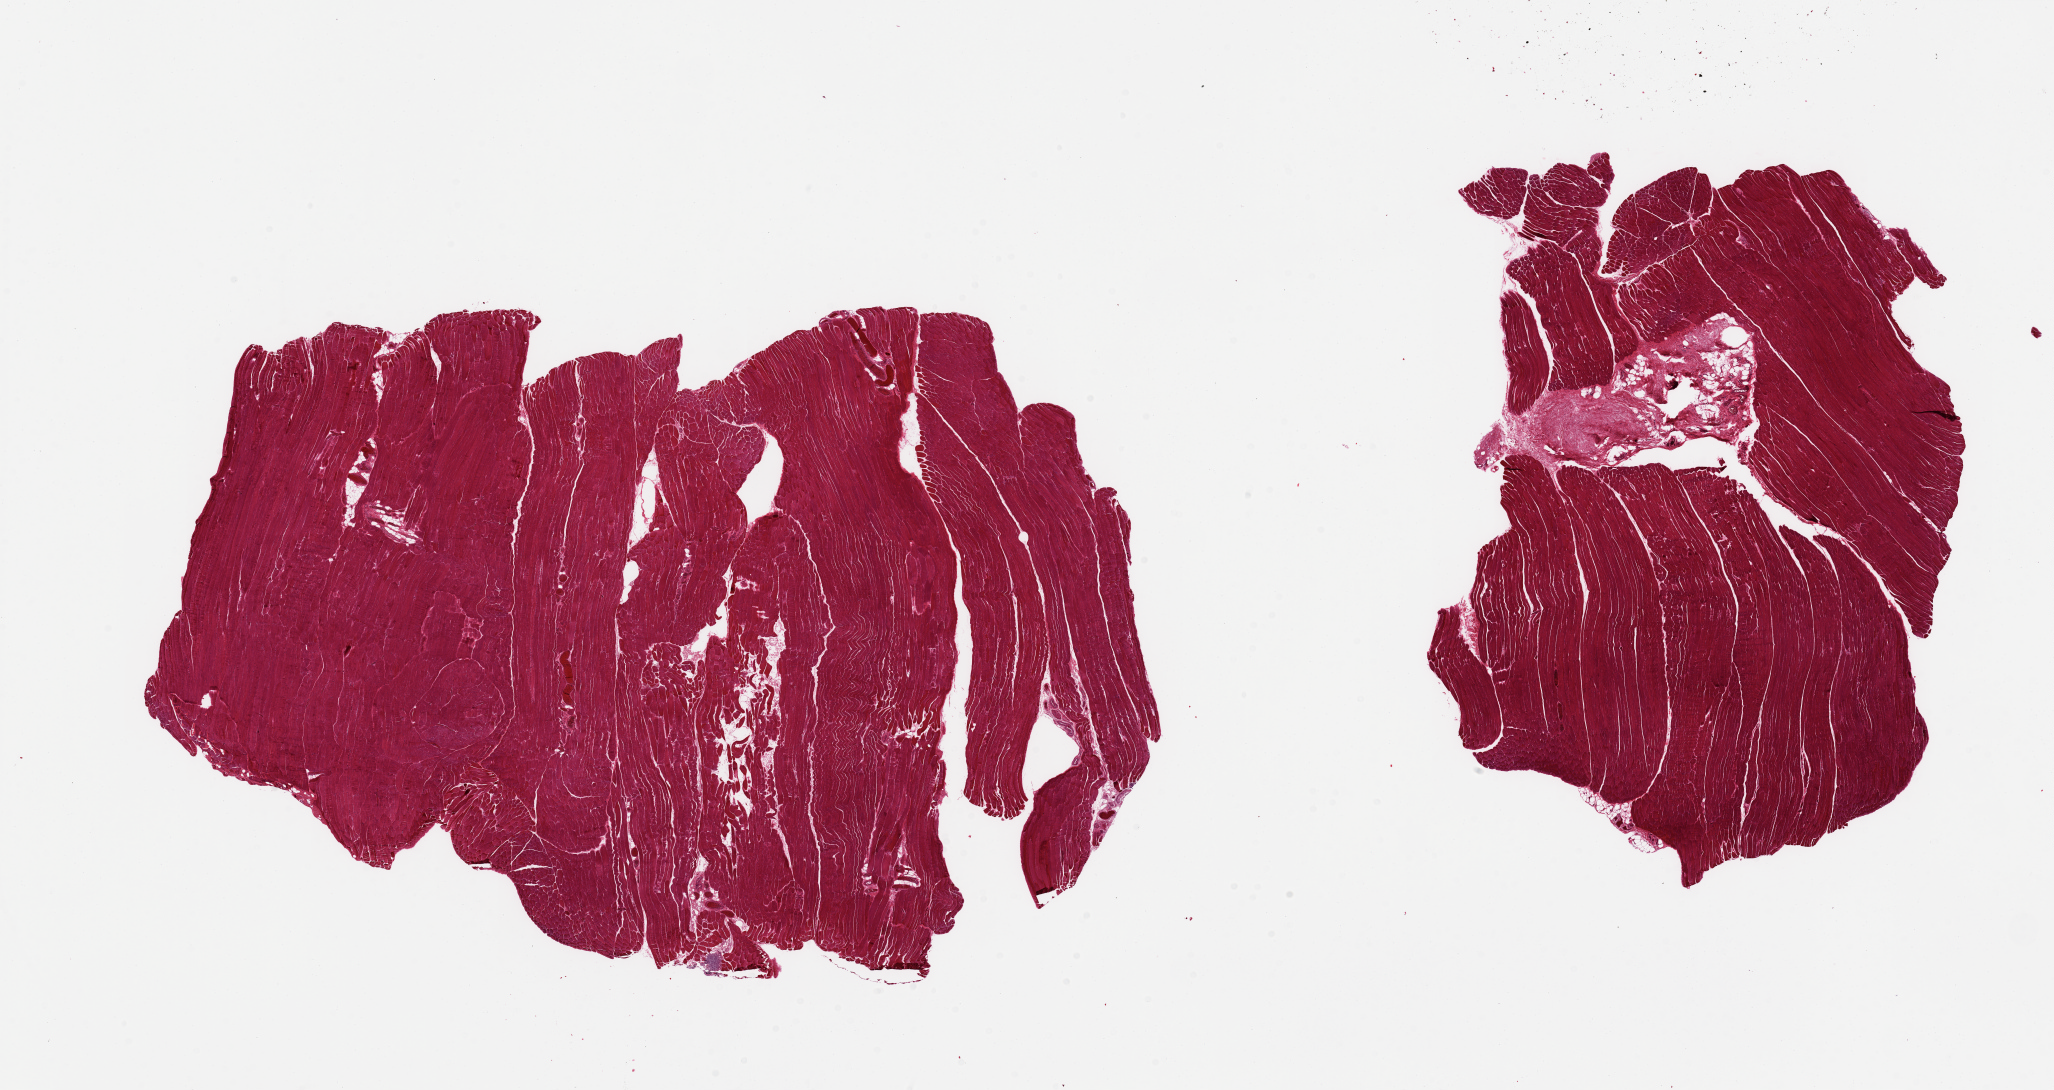
Digitized haematoxylin and eosin-stained section, shown as a low-resolution overview of the whole scanned area (about 32.5 x 17.2 mm). PAXgene-fixed, paraffin-embedded tissue. Section of skeletal muscle (target tissue). Donor tissue sample.
* reviewer comment on this tissue sample: 2 pieces, ~5% of one piece is fibrous tissue